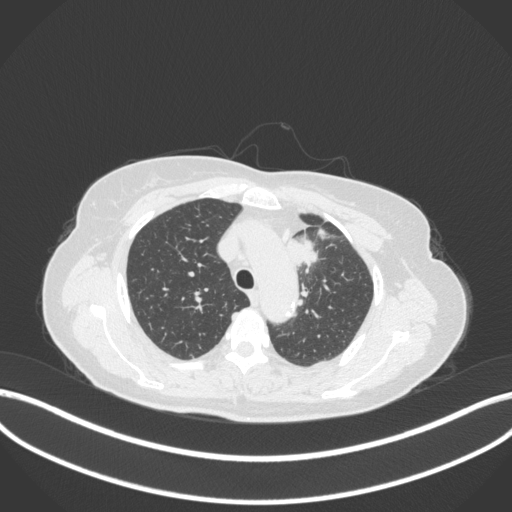
Chest CT, one axial slice. Slice 253 of 368 in the series (ordered by position). 120 kVp. Lung window (W 1500 / L -600 HU). 1 mm slice thickness. 512 × 512 image matrix. Patient: female, 65 years. From the clinical record (not read from this slice): clinical TNM (as recorded): T2a N0 M0; histopathological grade: G2-3.
Outlined on this slice (bounding box drawn by a radiologist):
- lung tumour (recorded histology: adenocarcinoma): box from (x=284, y=233) to (x=321, y=270) px